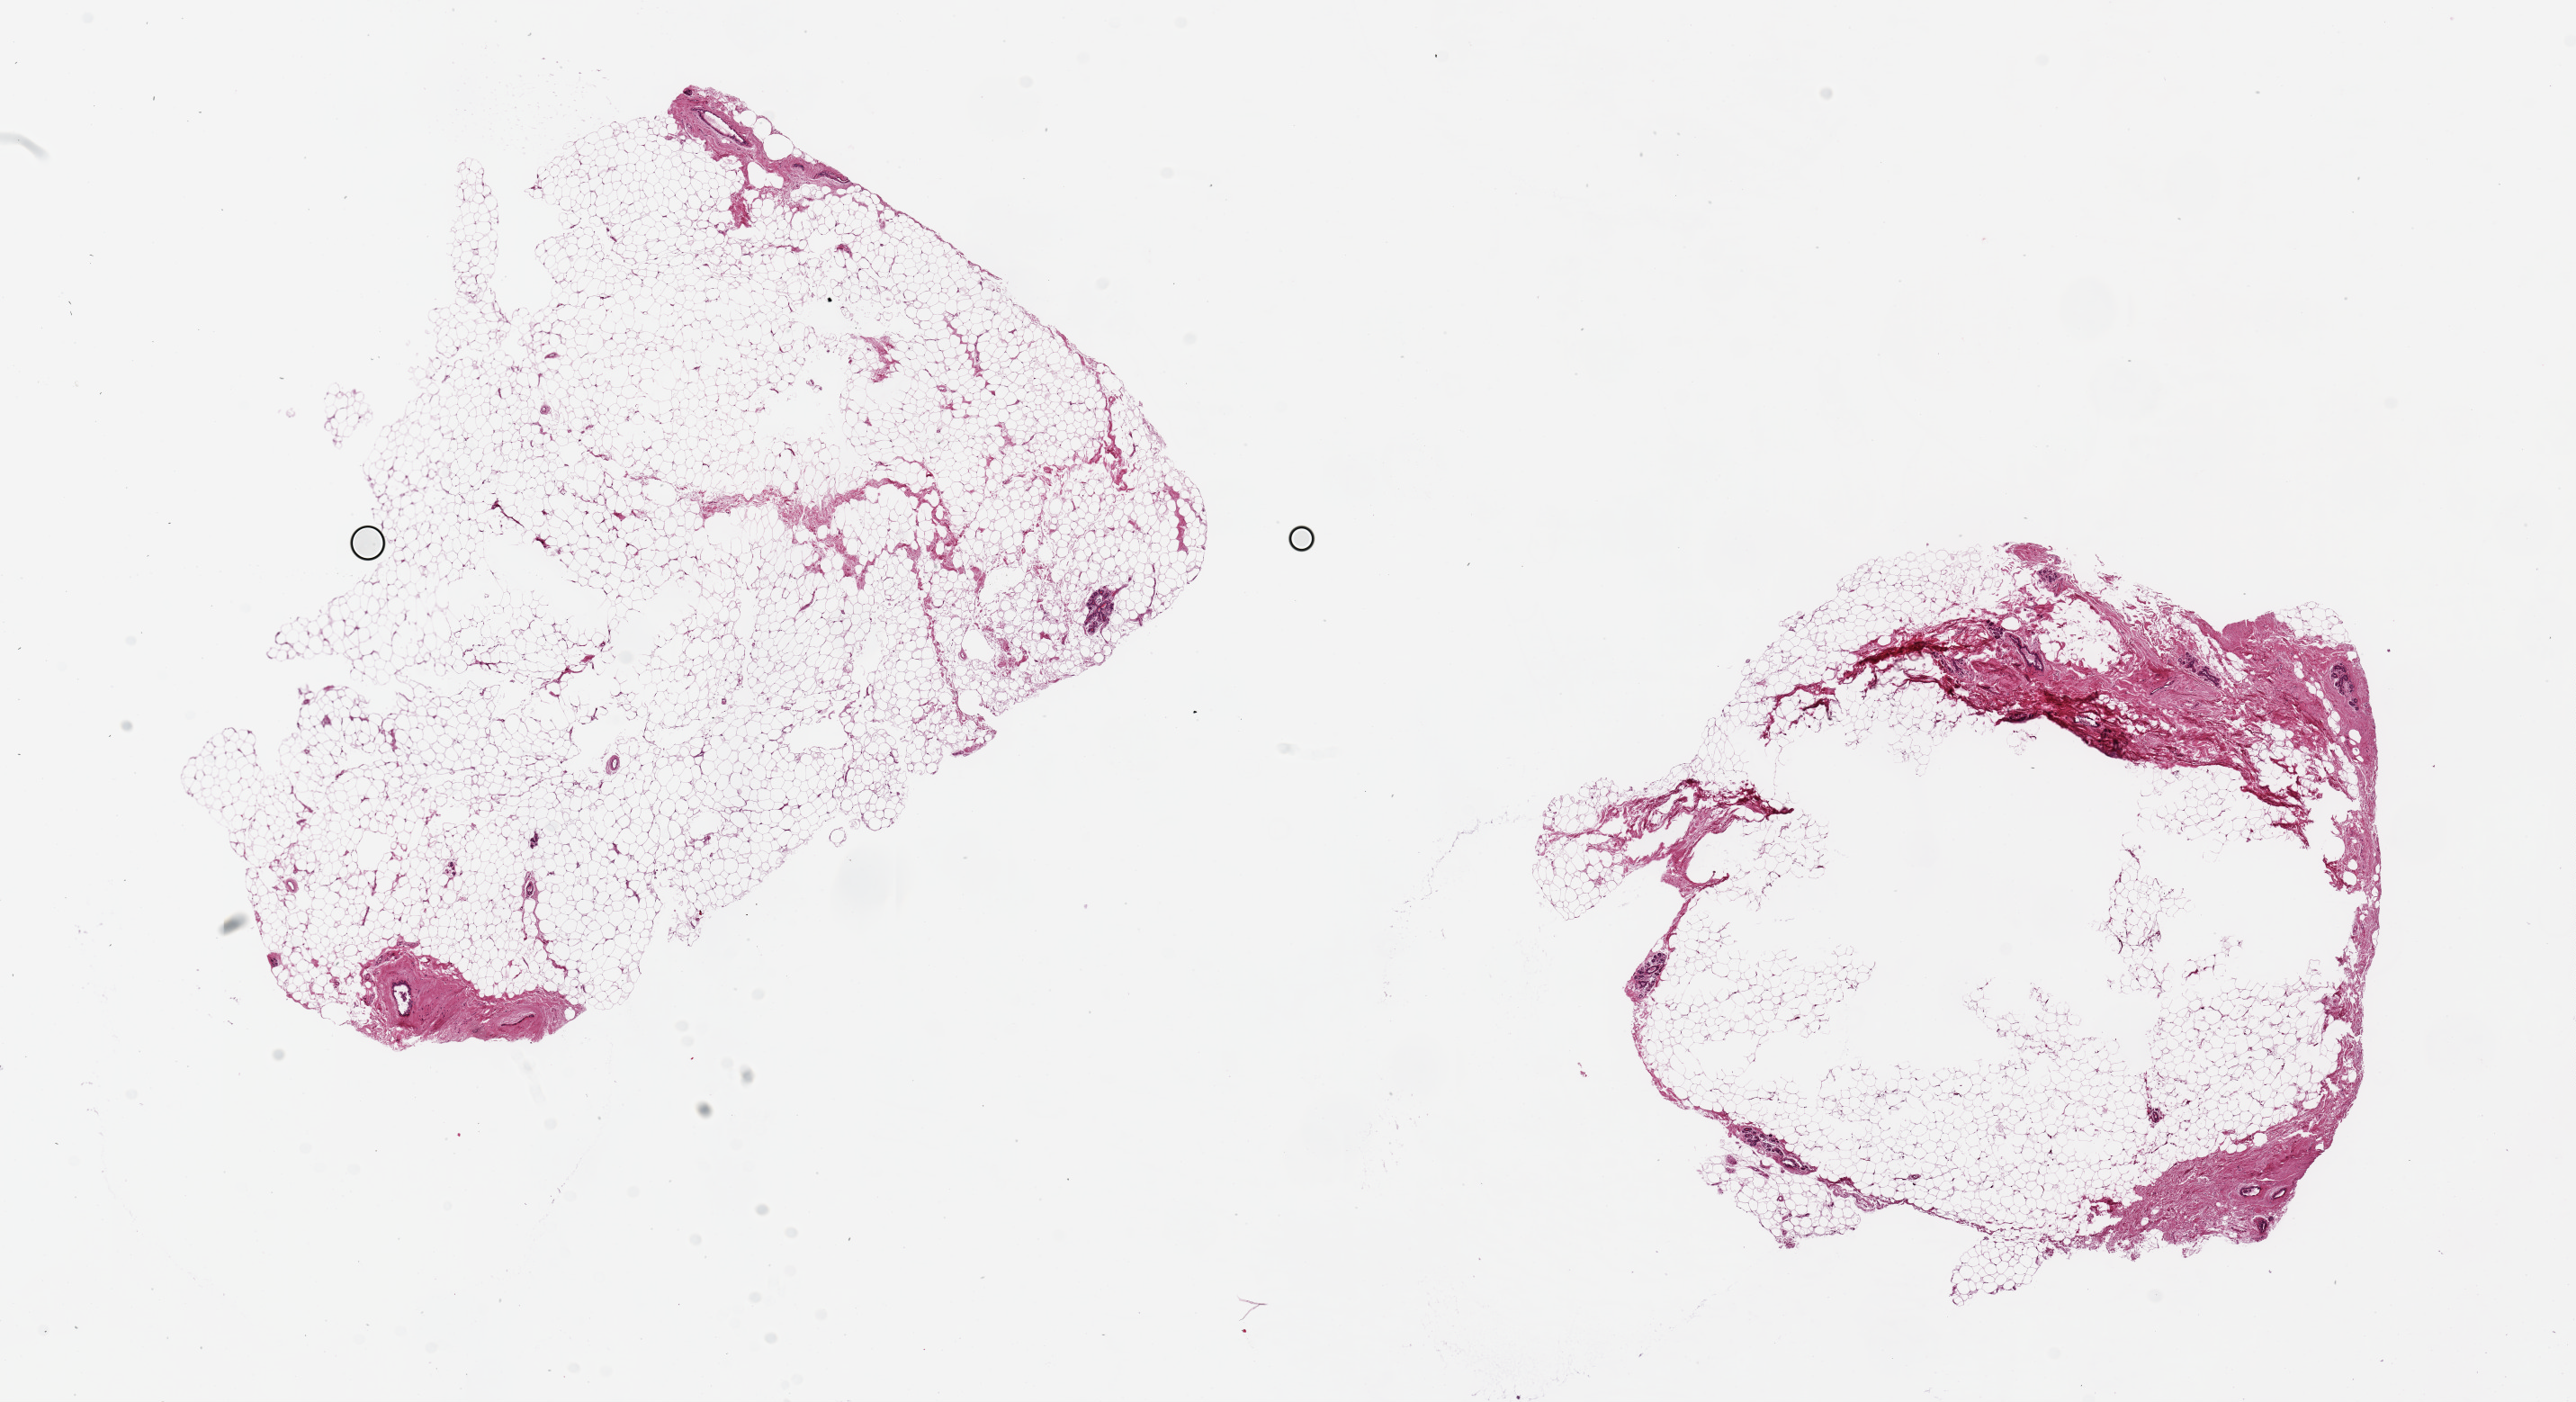
Digitized hematoxylin and eosin (H&E)-stained section — a low-resolution overview of the entire scanned area, about 22.6 x 12.3 mm (acquisition: 20x scan), PAXgene-fixed, paraffin-embedded tissue, target tissue: breast, tissue donor sample. Donor sex: female.
- review note (as recorded): 2 pieces, 7x6 & 9x6.5mm; small number of lobules and ~90% adipose